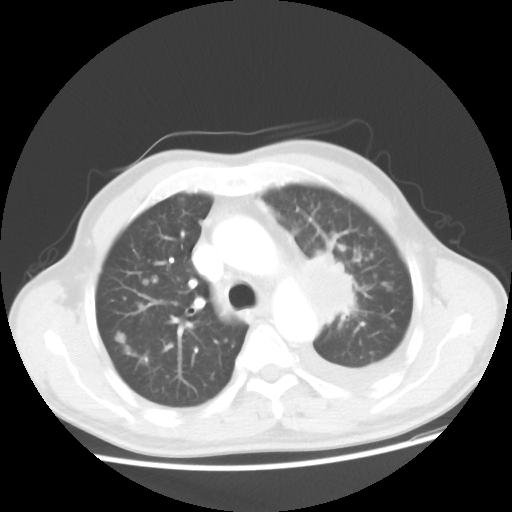
Chest CT, one axial slice. Slice 33 of 48 in the series (ordered by position). Reconstruction kernel STANDARD. Lung window (W 1500 / L -600 HU). 5 mm slice thickness. 512 × 512 image matrix, field of view 362 × 362 mm. Male patient, age 55 years. Case-level facts recorded for this patient, not image findings: clinical TNM (as recorded): T2 N3 M1a.
Outlined on this slice (bounding box drawn by a radiologist):
- lung tumour (recorded histology: squamous cell carcinoma): box from (x=305, y=252) to (x=358, y=330) px